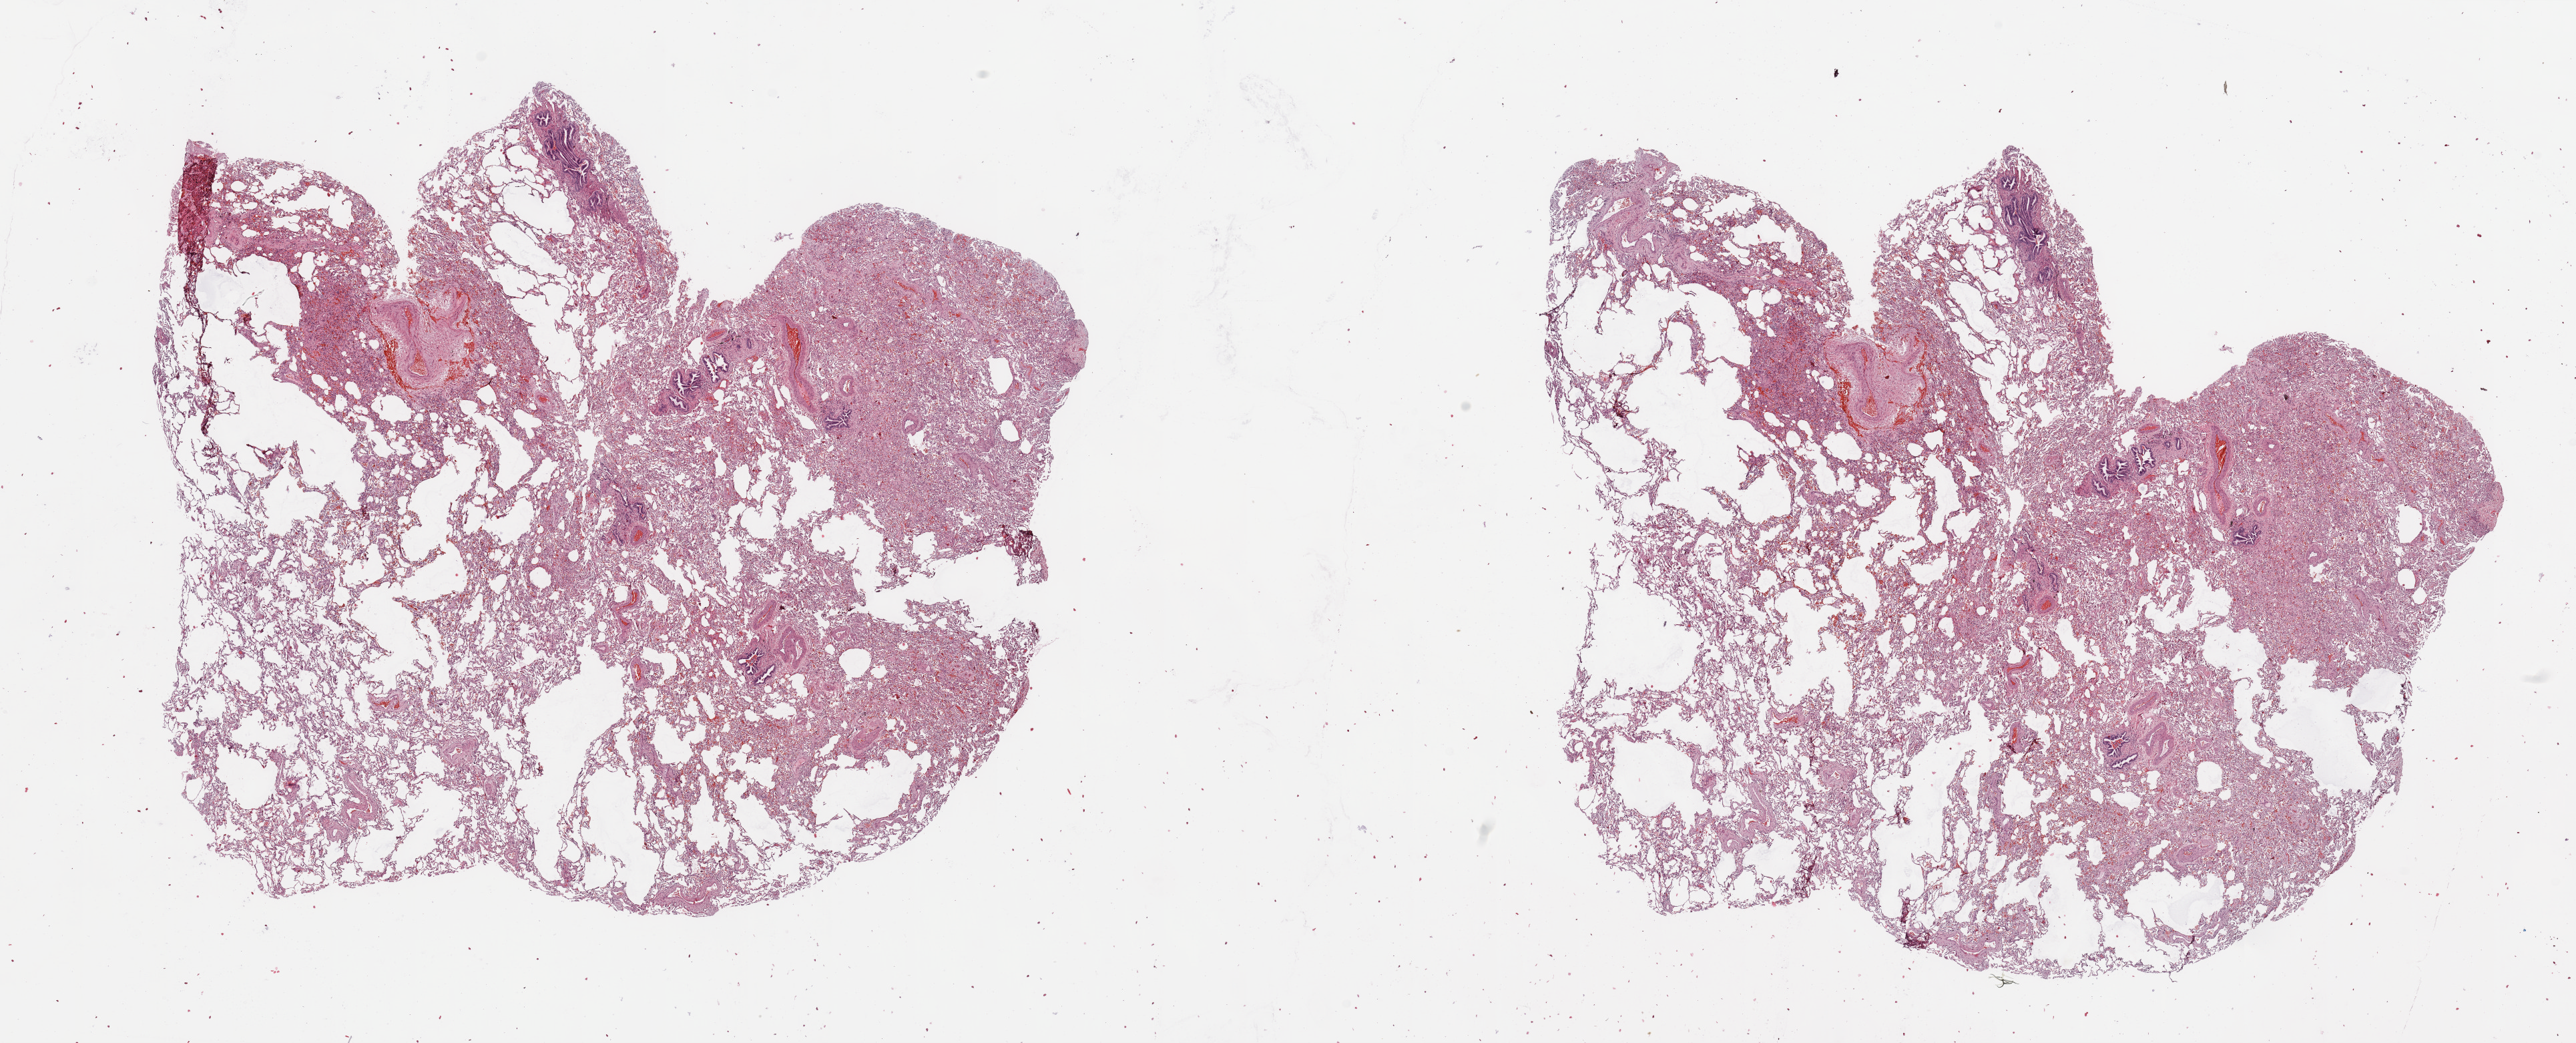
Hematoxylin and eosin (H&E) stained whole-slide image, low-resolution overview of the scanned area, about 30.5 x 12.4 mm (from a 20x scan). Normal (non-tumour) tissue sample, sampled site: lung. Female, 67 y/o.
• this section: normal (non-tumour) tissue from the same patient
• patient diagnosis: Adenocarcinoma, NOS